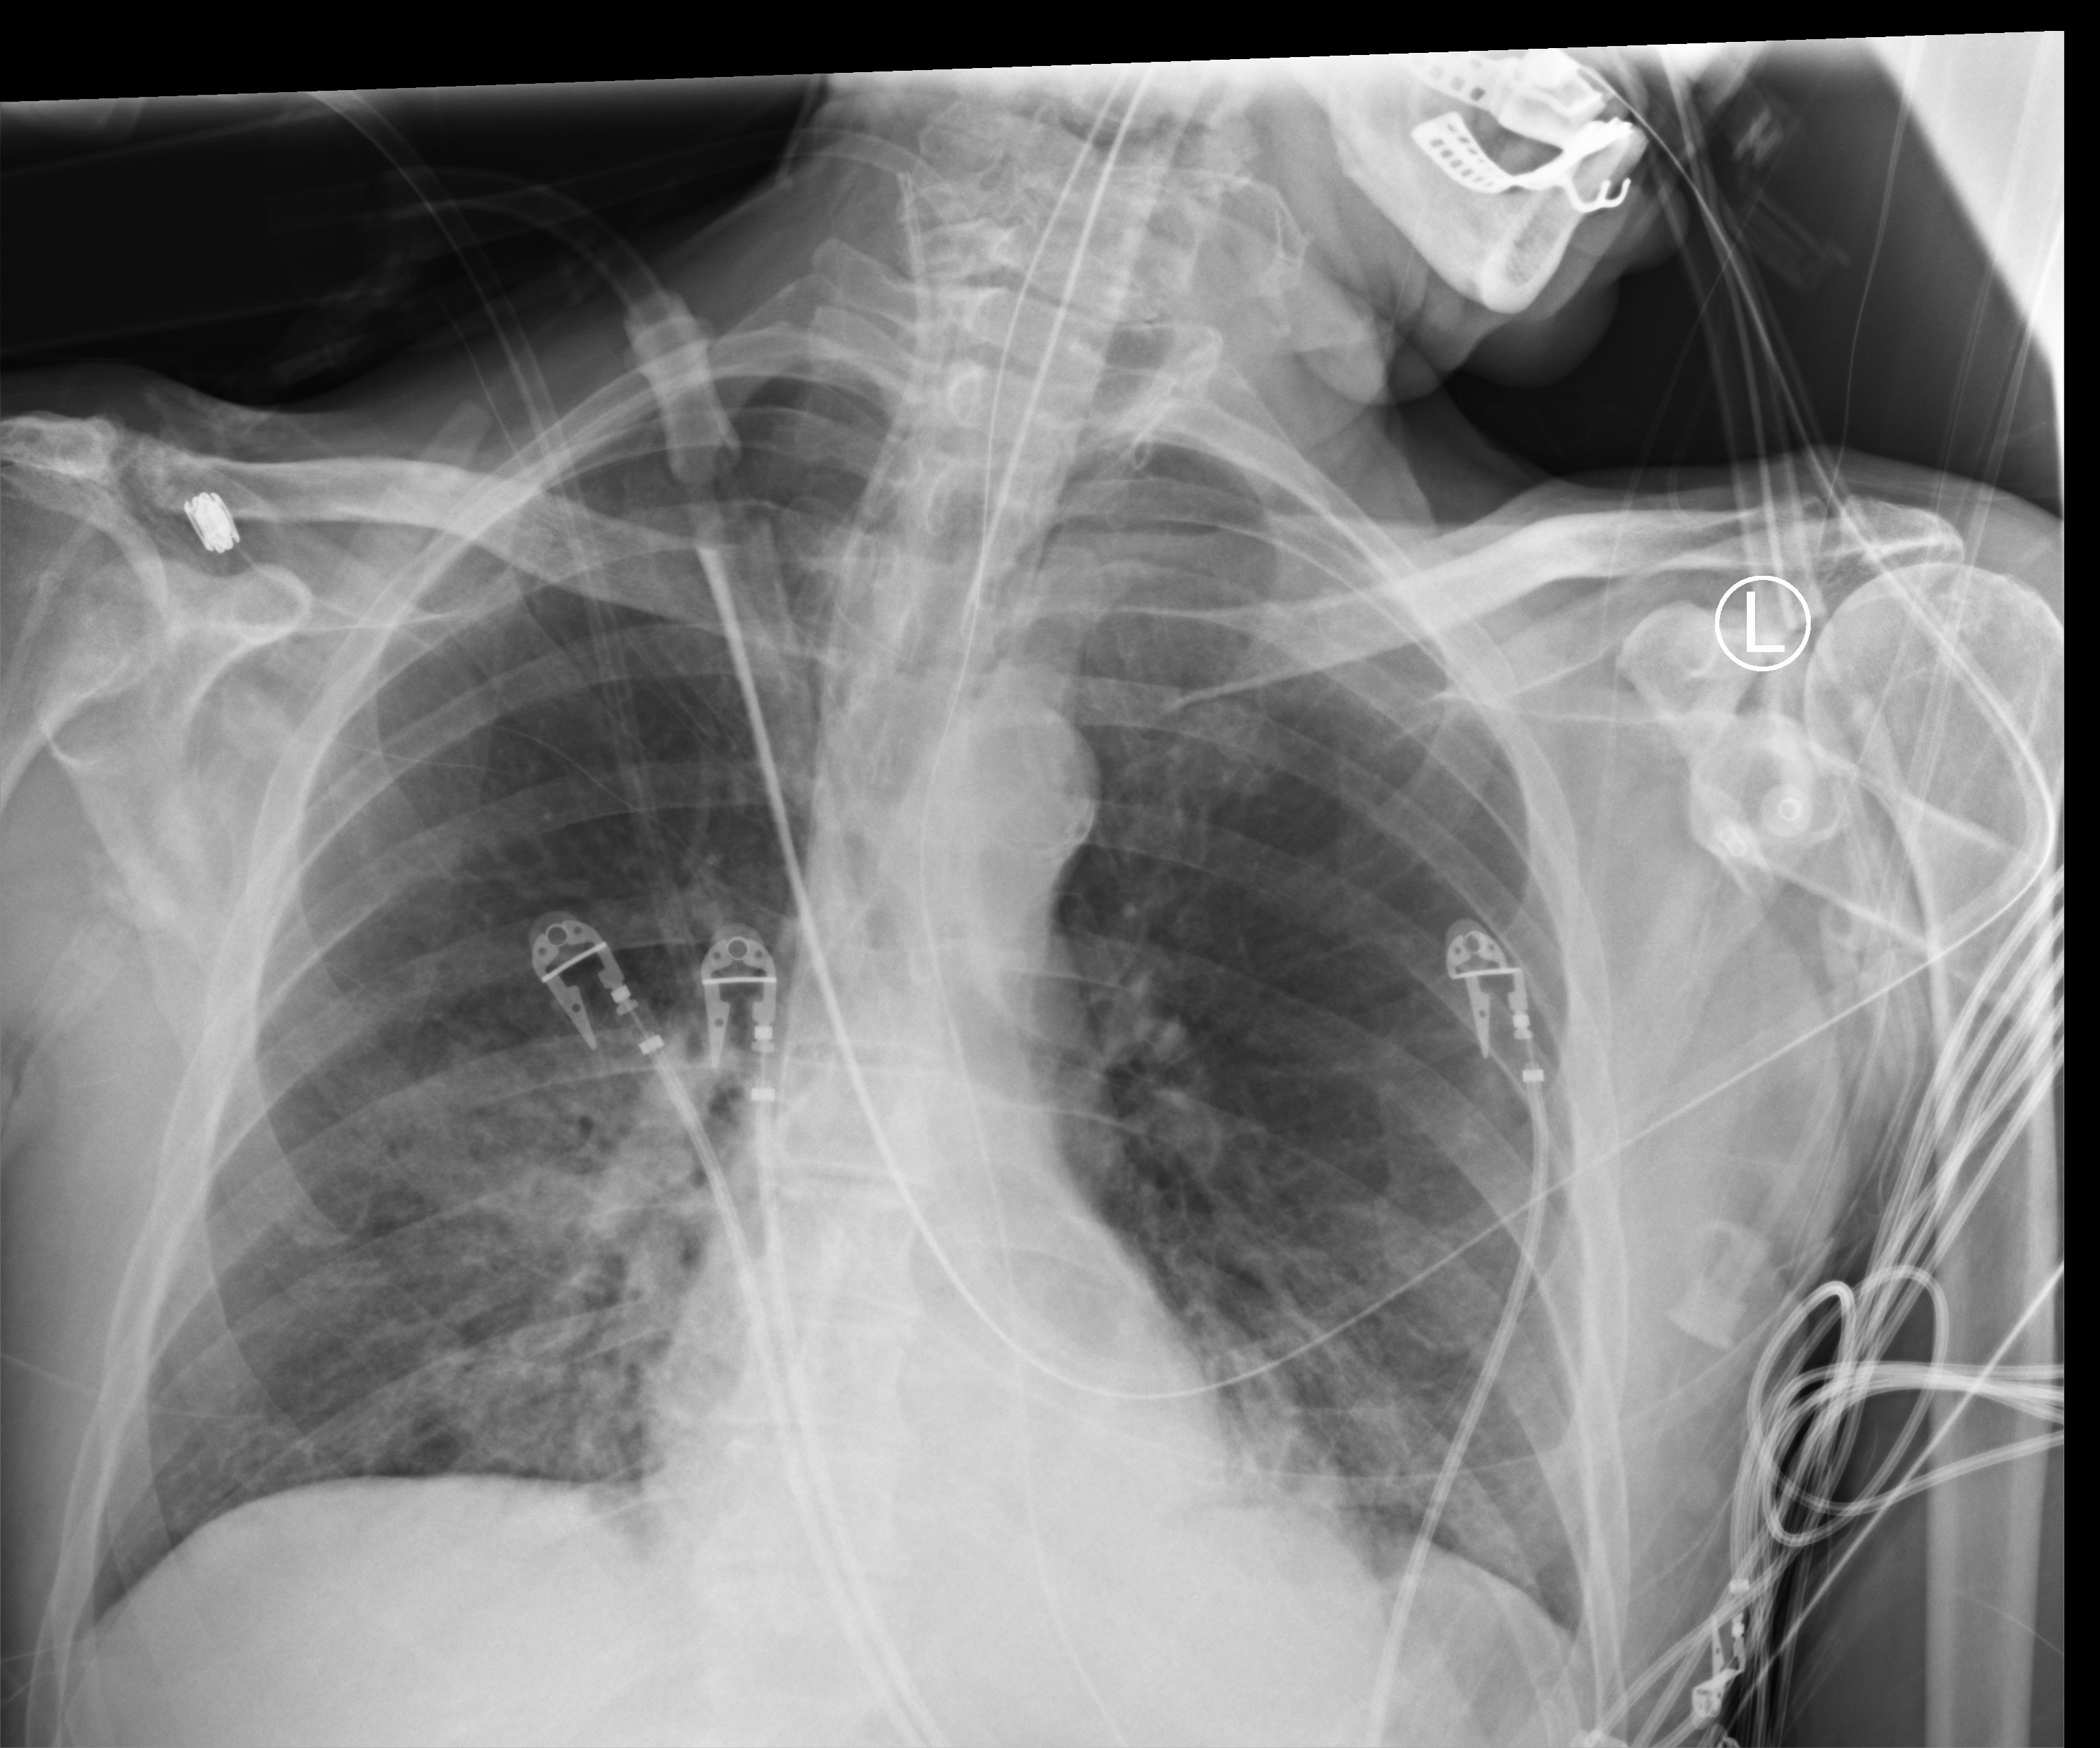
Portable chest radiograph; anteroposterior (AP) projection. Male patient hospitalised with COVID-19, age 75–90 years.
From the hospital-stay record, not from the radiograph (when in the stay this image was taken is not recorded): mechanically ventilated during this hospital stay: yes; COPD (admission record): no.